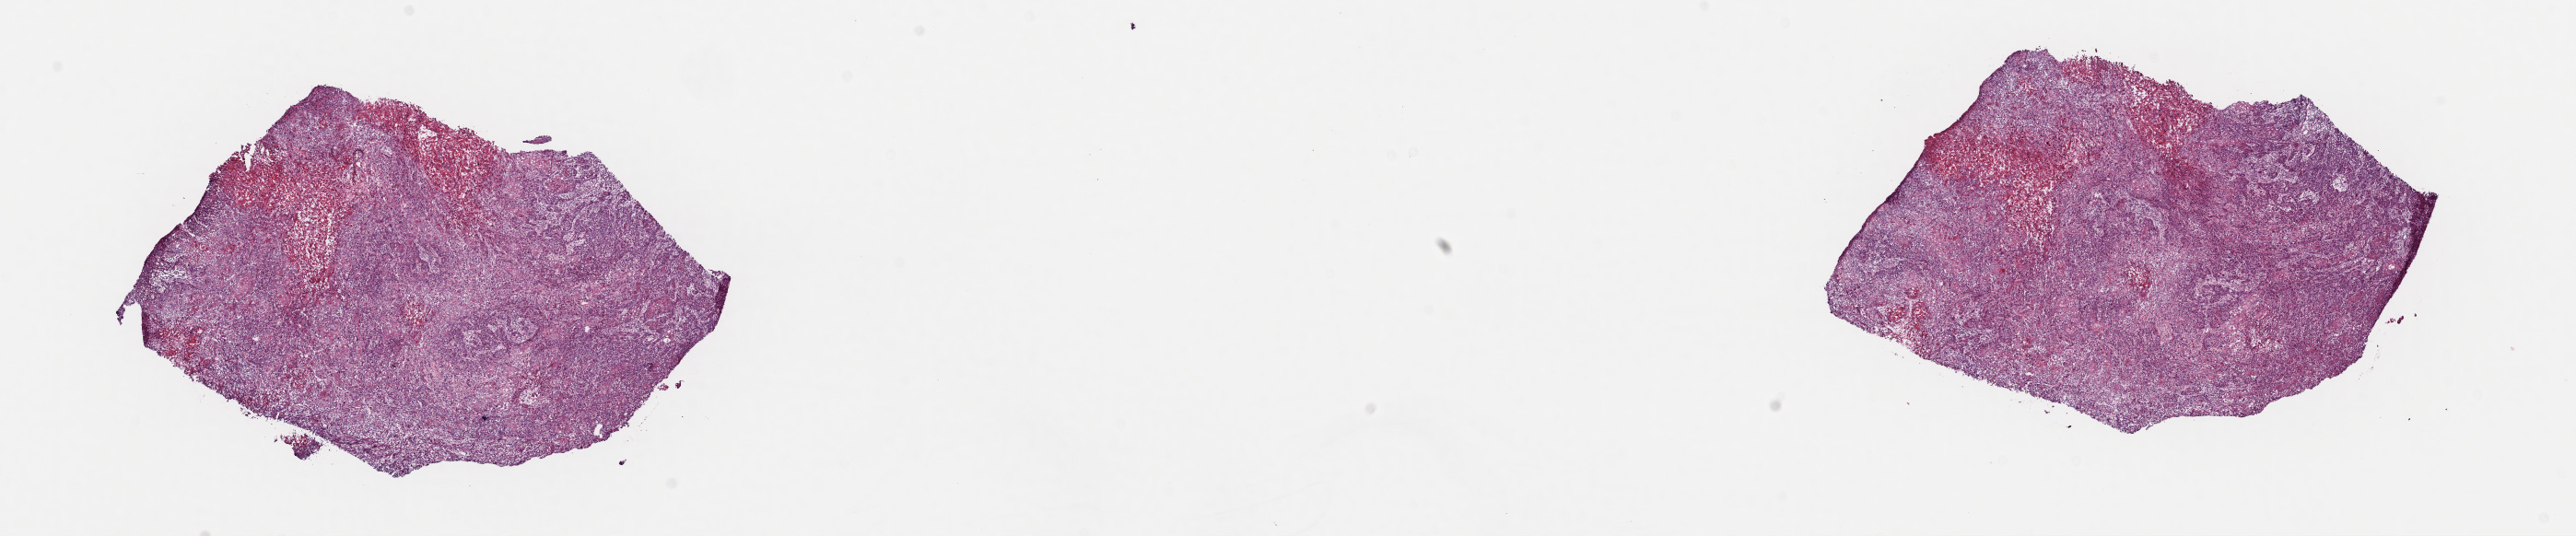
Whole-slide histology image, H&E, a low-resolution overview of the entire scanned area, about 22.1 x 4.6 mm (from a 40x scan); frozen section from the top of the tissue portion; sample: primary tumour, head and neck. Patient: male, age at initial diagnosis 74 years. Histologic grade: G2 (moderately differentiated). Slide review estimates, as recorded: tumour cells 70%, tumour nuclei 75%, normal cells 0%, stromal cells 20%, necrosis 10%. Inflammatory infiltration, as recorded: lymphocyte infiltration 10%, monocyte infiltration 0%, neutrophil infiltration 0%.
Histologic diagnosis: Squamous cell carcinoma, keratinizing, NOS (mouth, NOS). Laterality: left. AJCC pathologic stage: IVA (7th edition). TNM: T4a N0 MX.